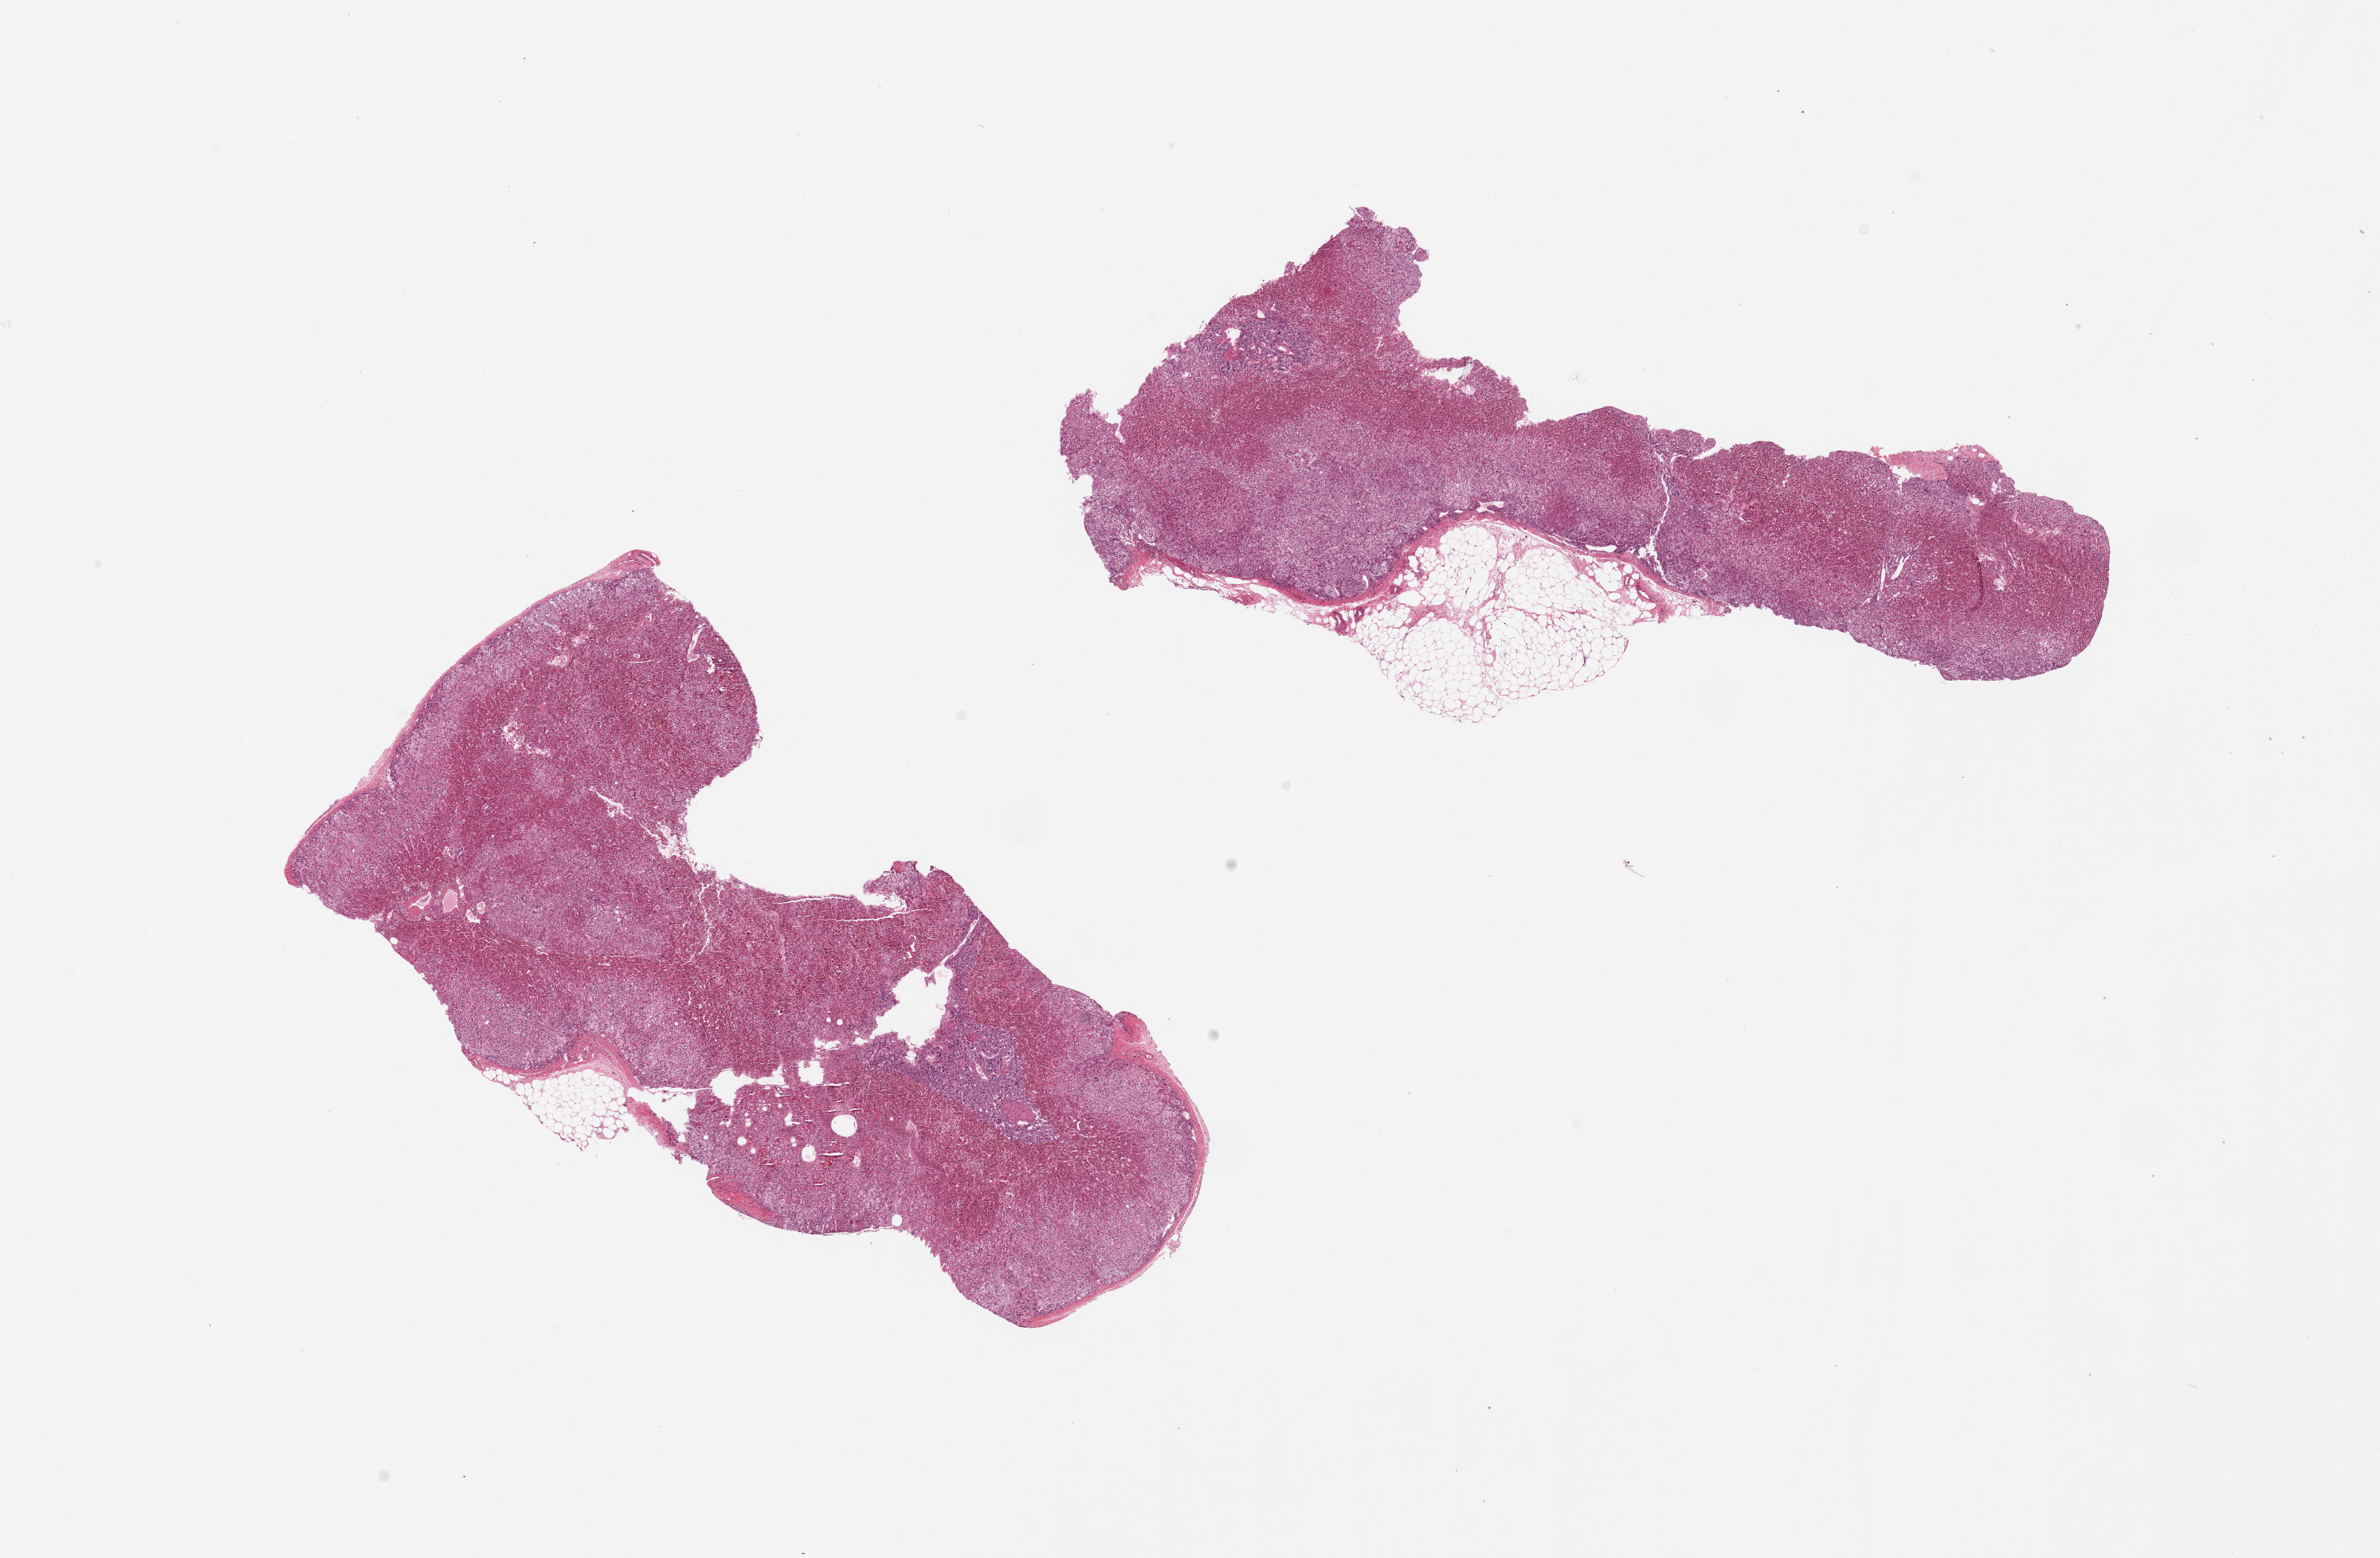
Whole-slide image, hematoxylin and eosin (H&E) stain, whole scanned area (about 23.6 x 15.5 mm) shown as a low-resolution overview, PAXgene-fixed paraffin-embedded (PFPE) section, section of adrenal gland (target tissue), donor tissue sample. Male donor.
- review note (as recorded): 2 pieces, 25% peripheral fat on 1; 5% fat on other